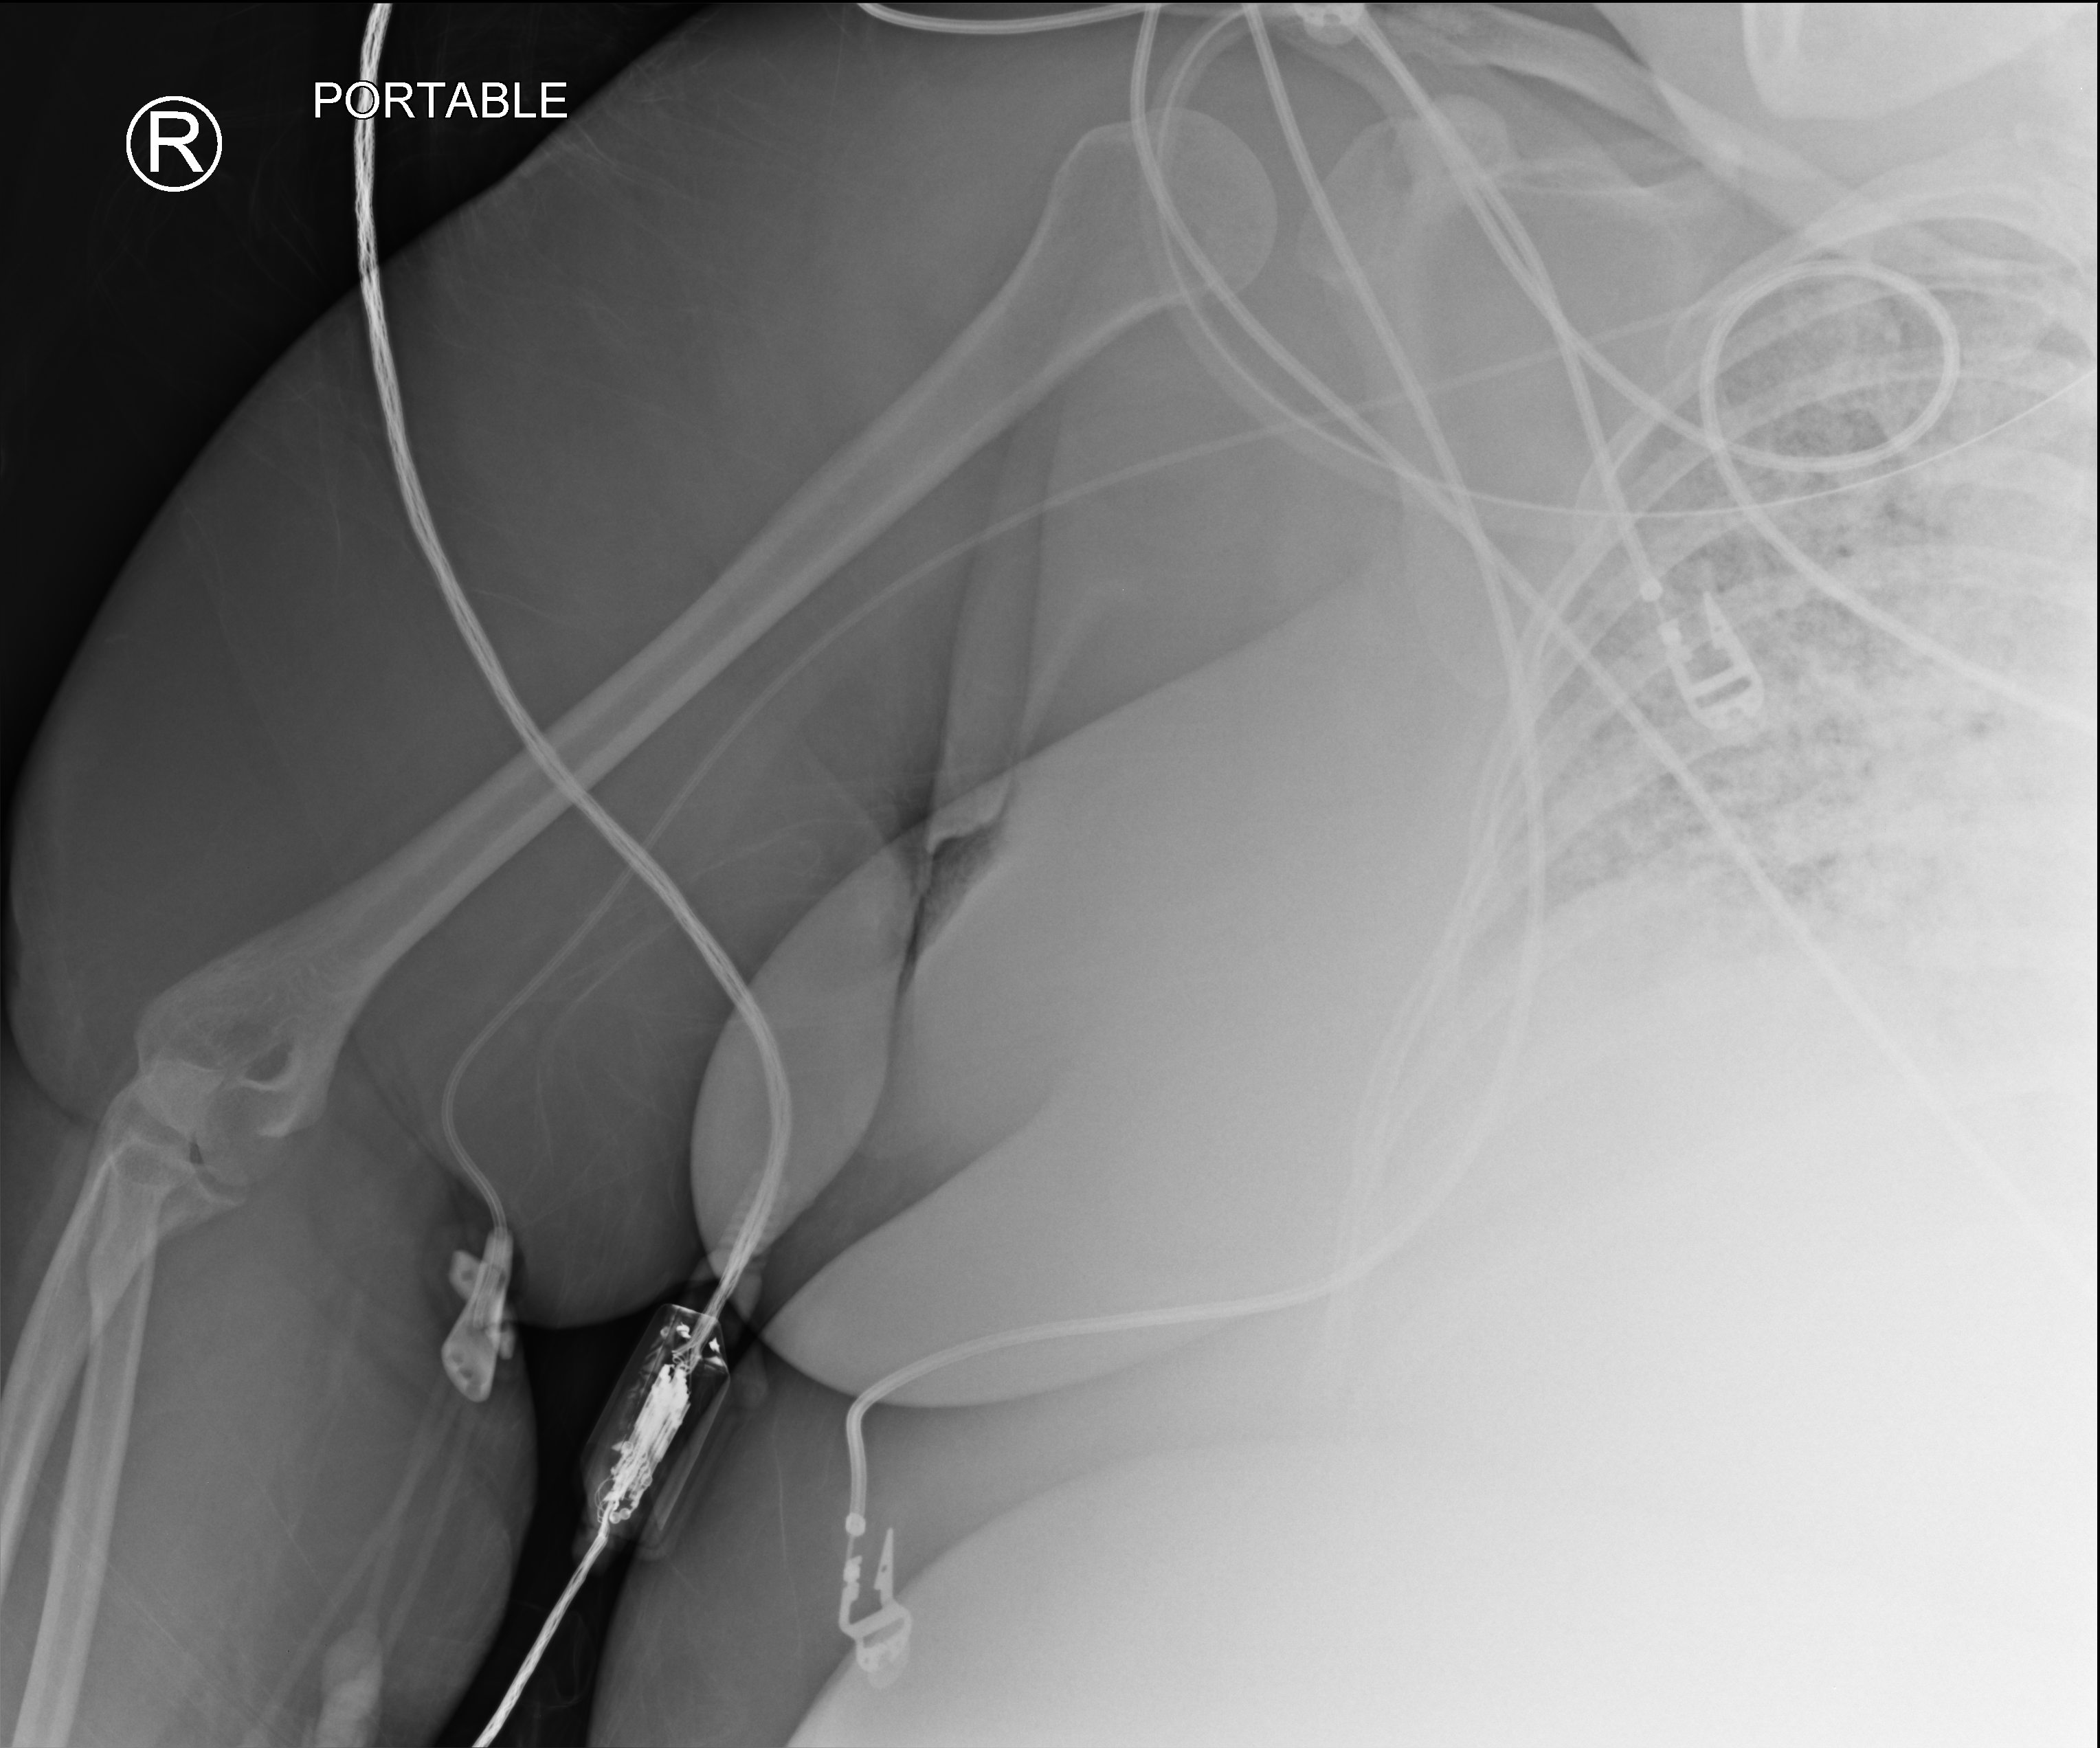
Chest X-ray (portable); anteroposterior (AP) projection. Patient hospitalised with COVID-19; female, aged 18–59 years.
Admission-level facts for this patient (not findings on this image; timing relative to this image not recorded):
- mechanically ventilated during this hospital stay: yes
- other chronic lung disease (admission record): no
- COPD (admission record): no